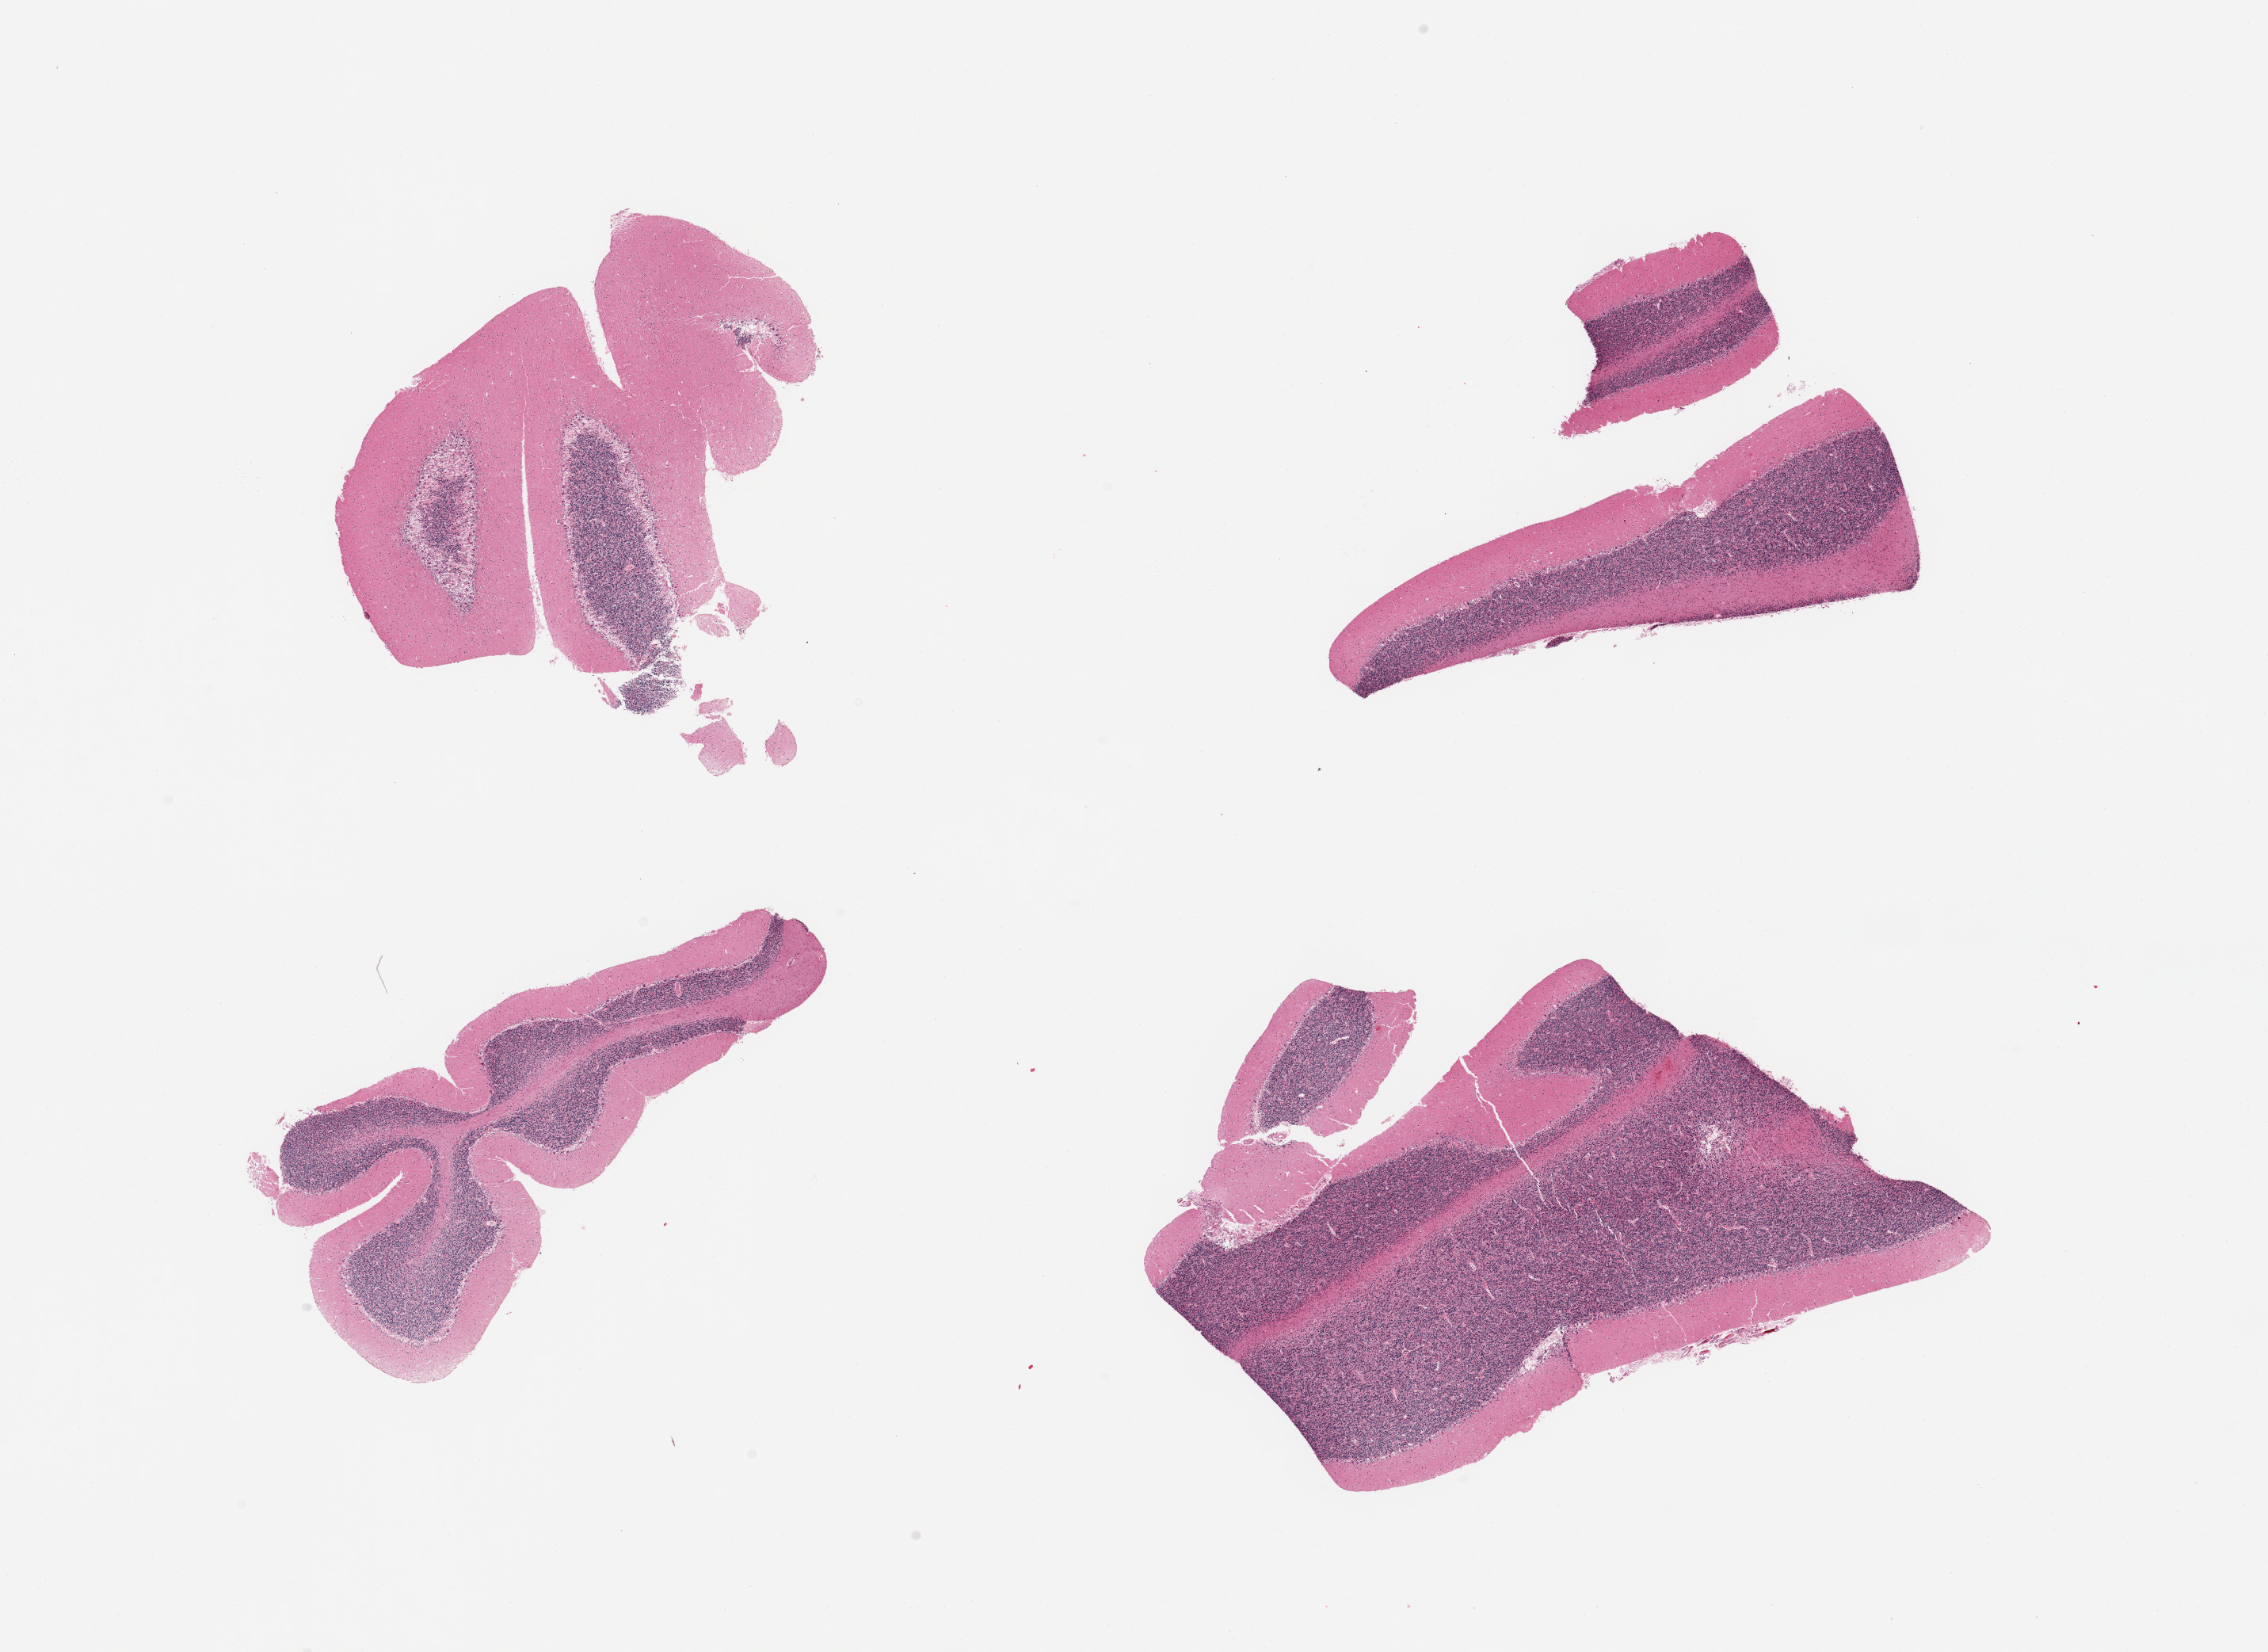
H&E whole-slide image, low-resolution overview of the scanned area, about 22.6 x 16.5 mm, PAXgene-fixed paraffin-embedded (PFPE) section, section of cerebellum (target tissue), donor tissue sample. Donor sex: female.
* pathologist's review note for this sample: 4 pieces; purkinje cells present, mild to moderate autolysis